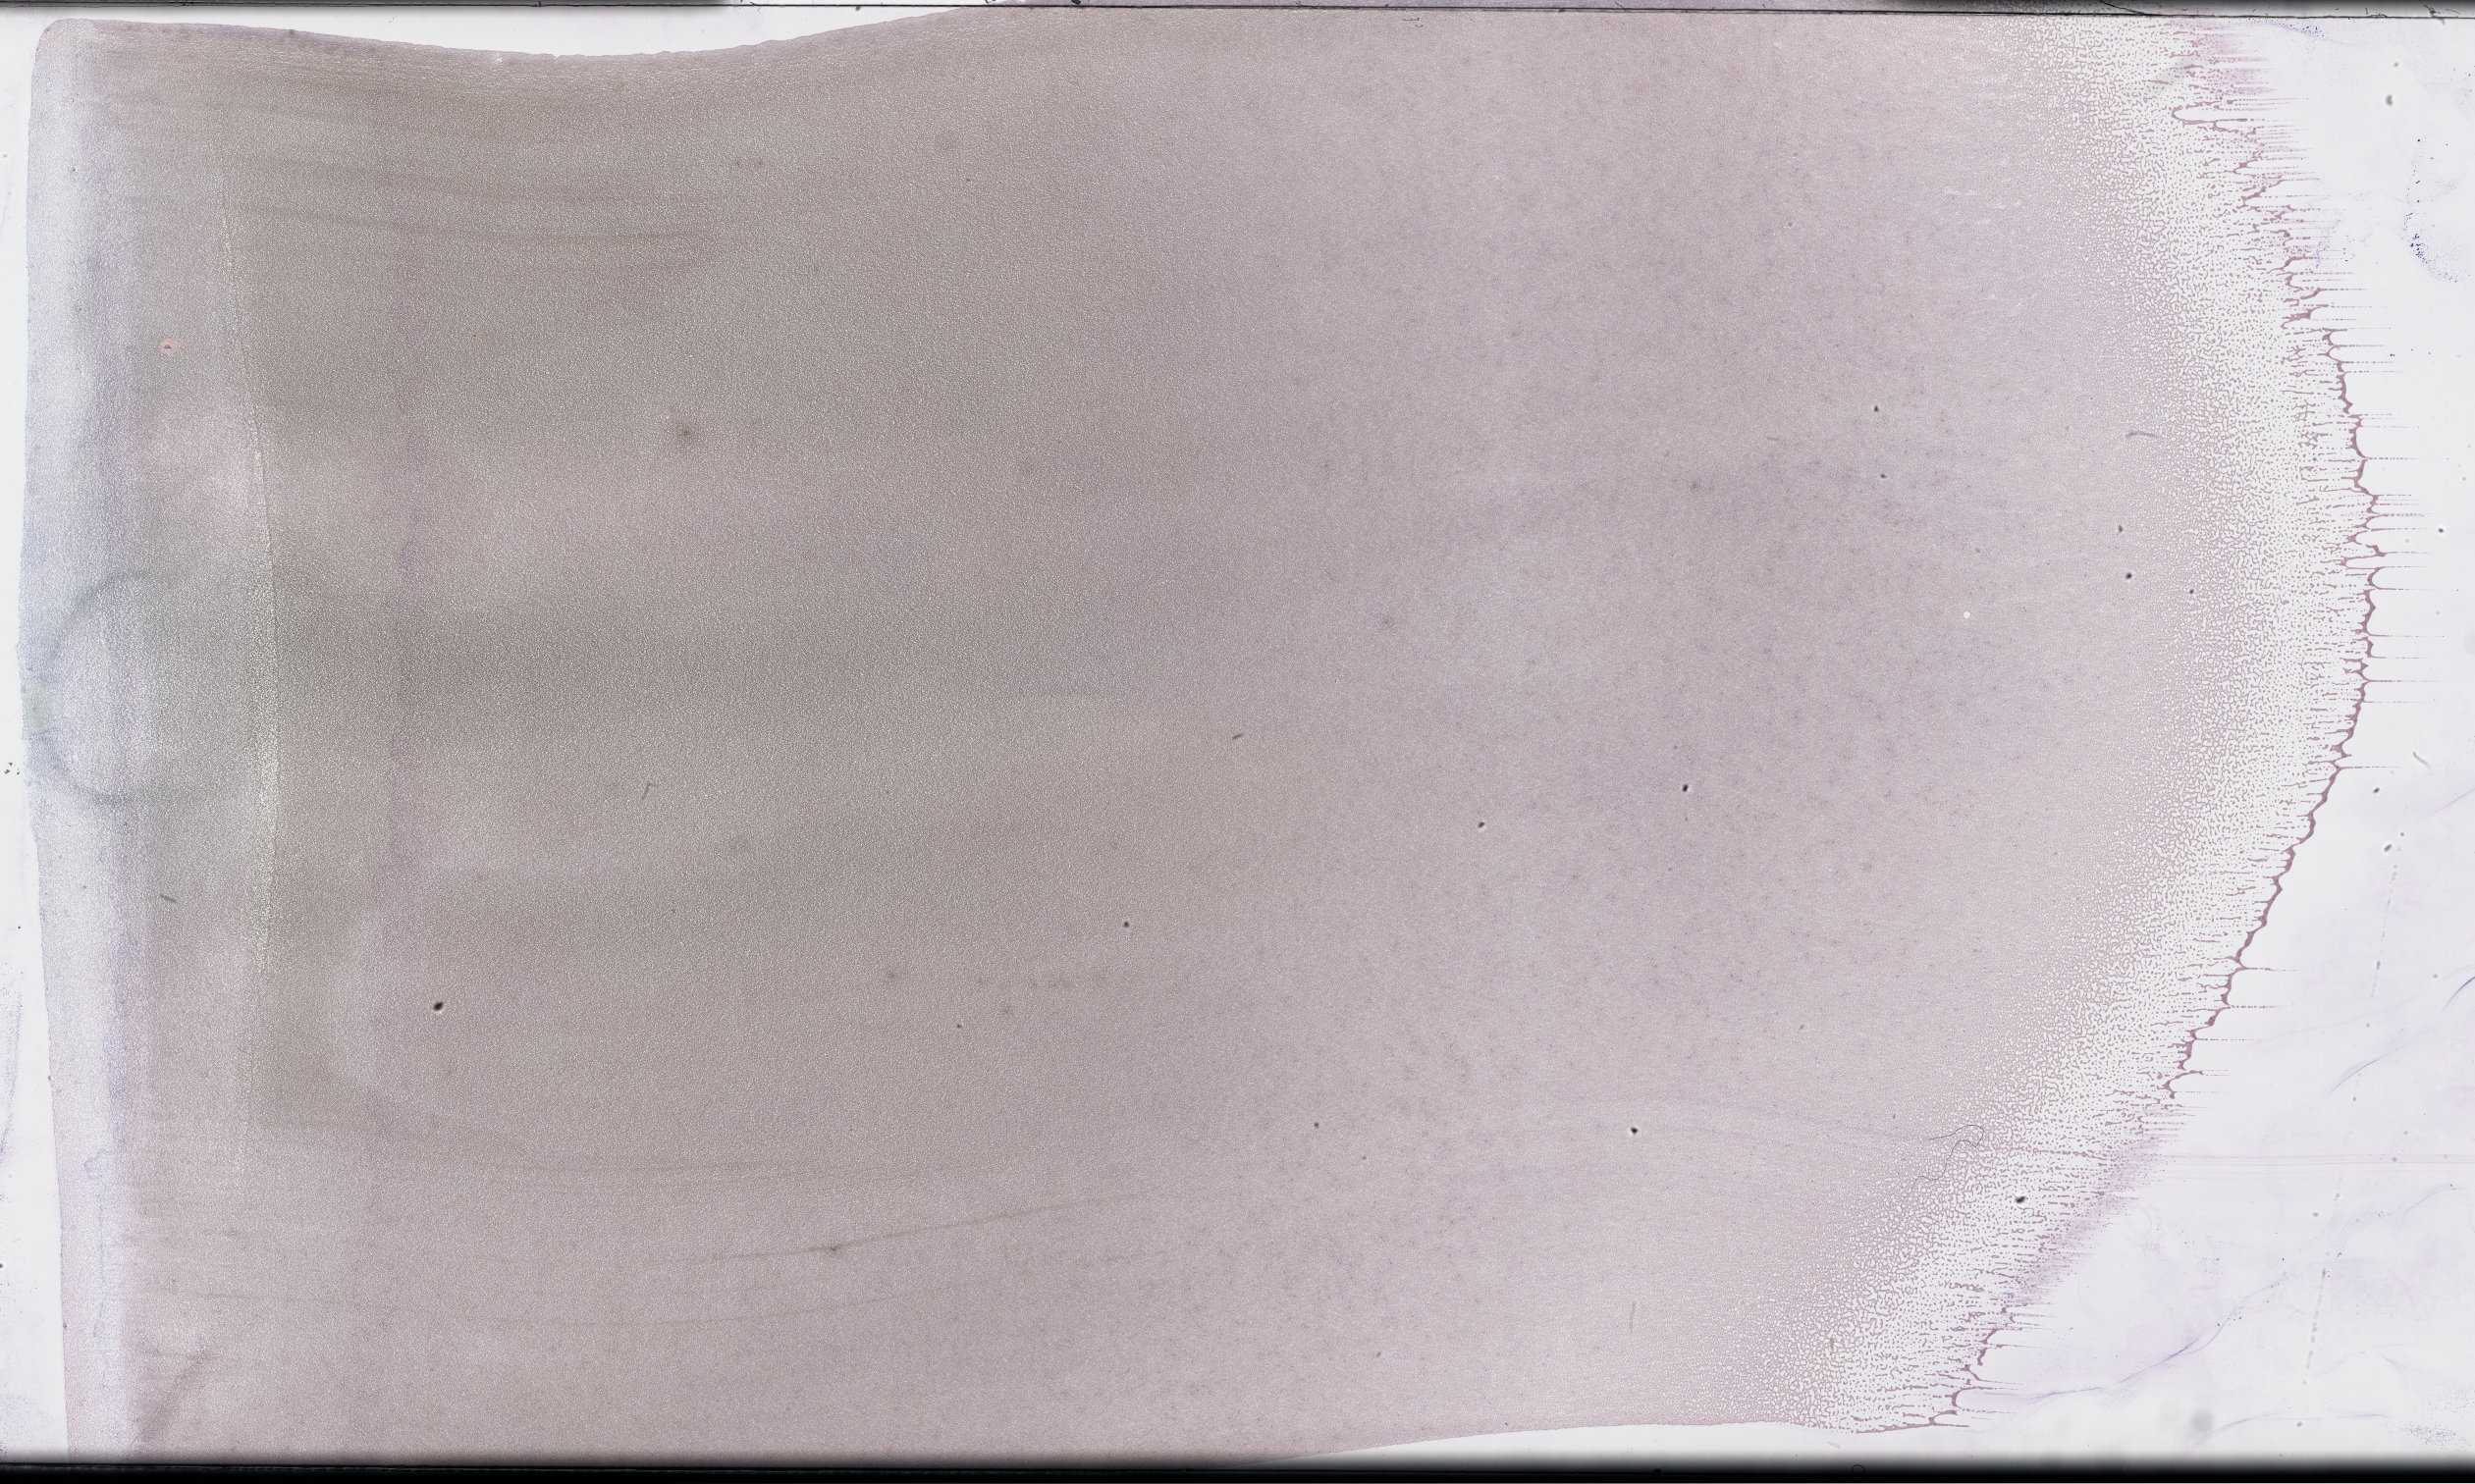
Whole-slide image of a whole blood smear, Wright–Giemsa stain, shown as a low-resolution overview of the whole scanned area (about 40.7 x 24.4 mm). Smear from an EDTA sample. Patient: male.
From a patient with: Plasma Cell Myeloma.